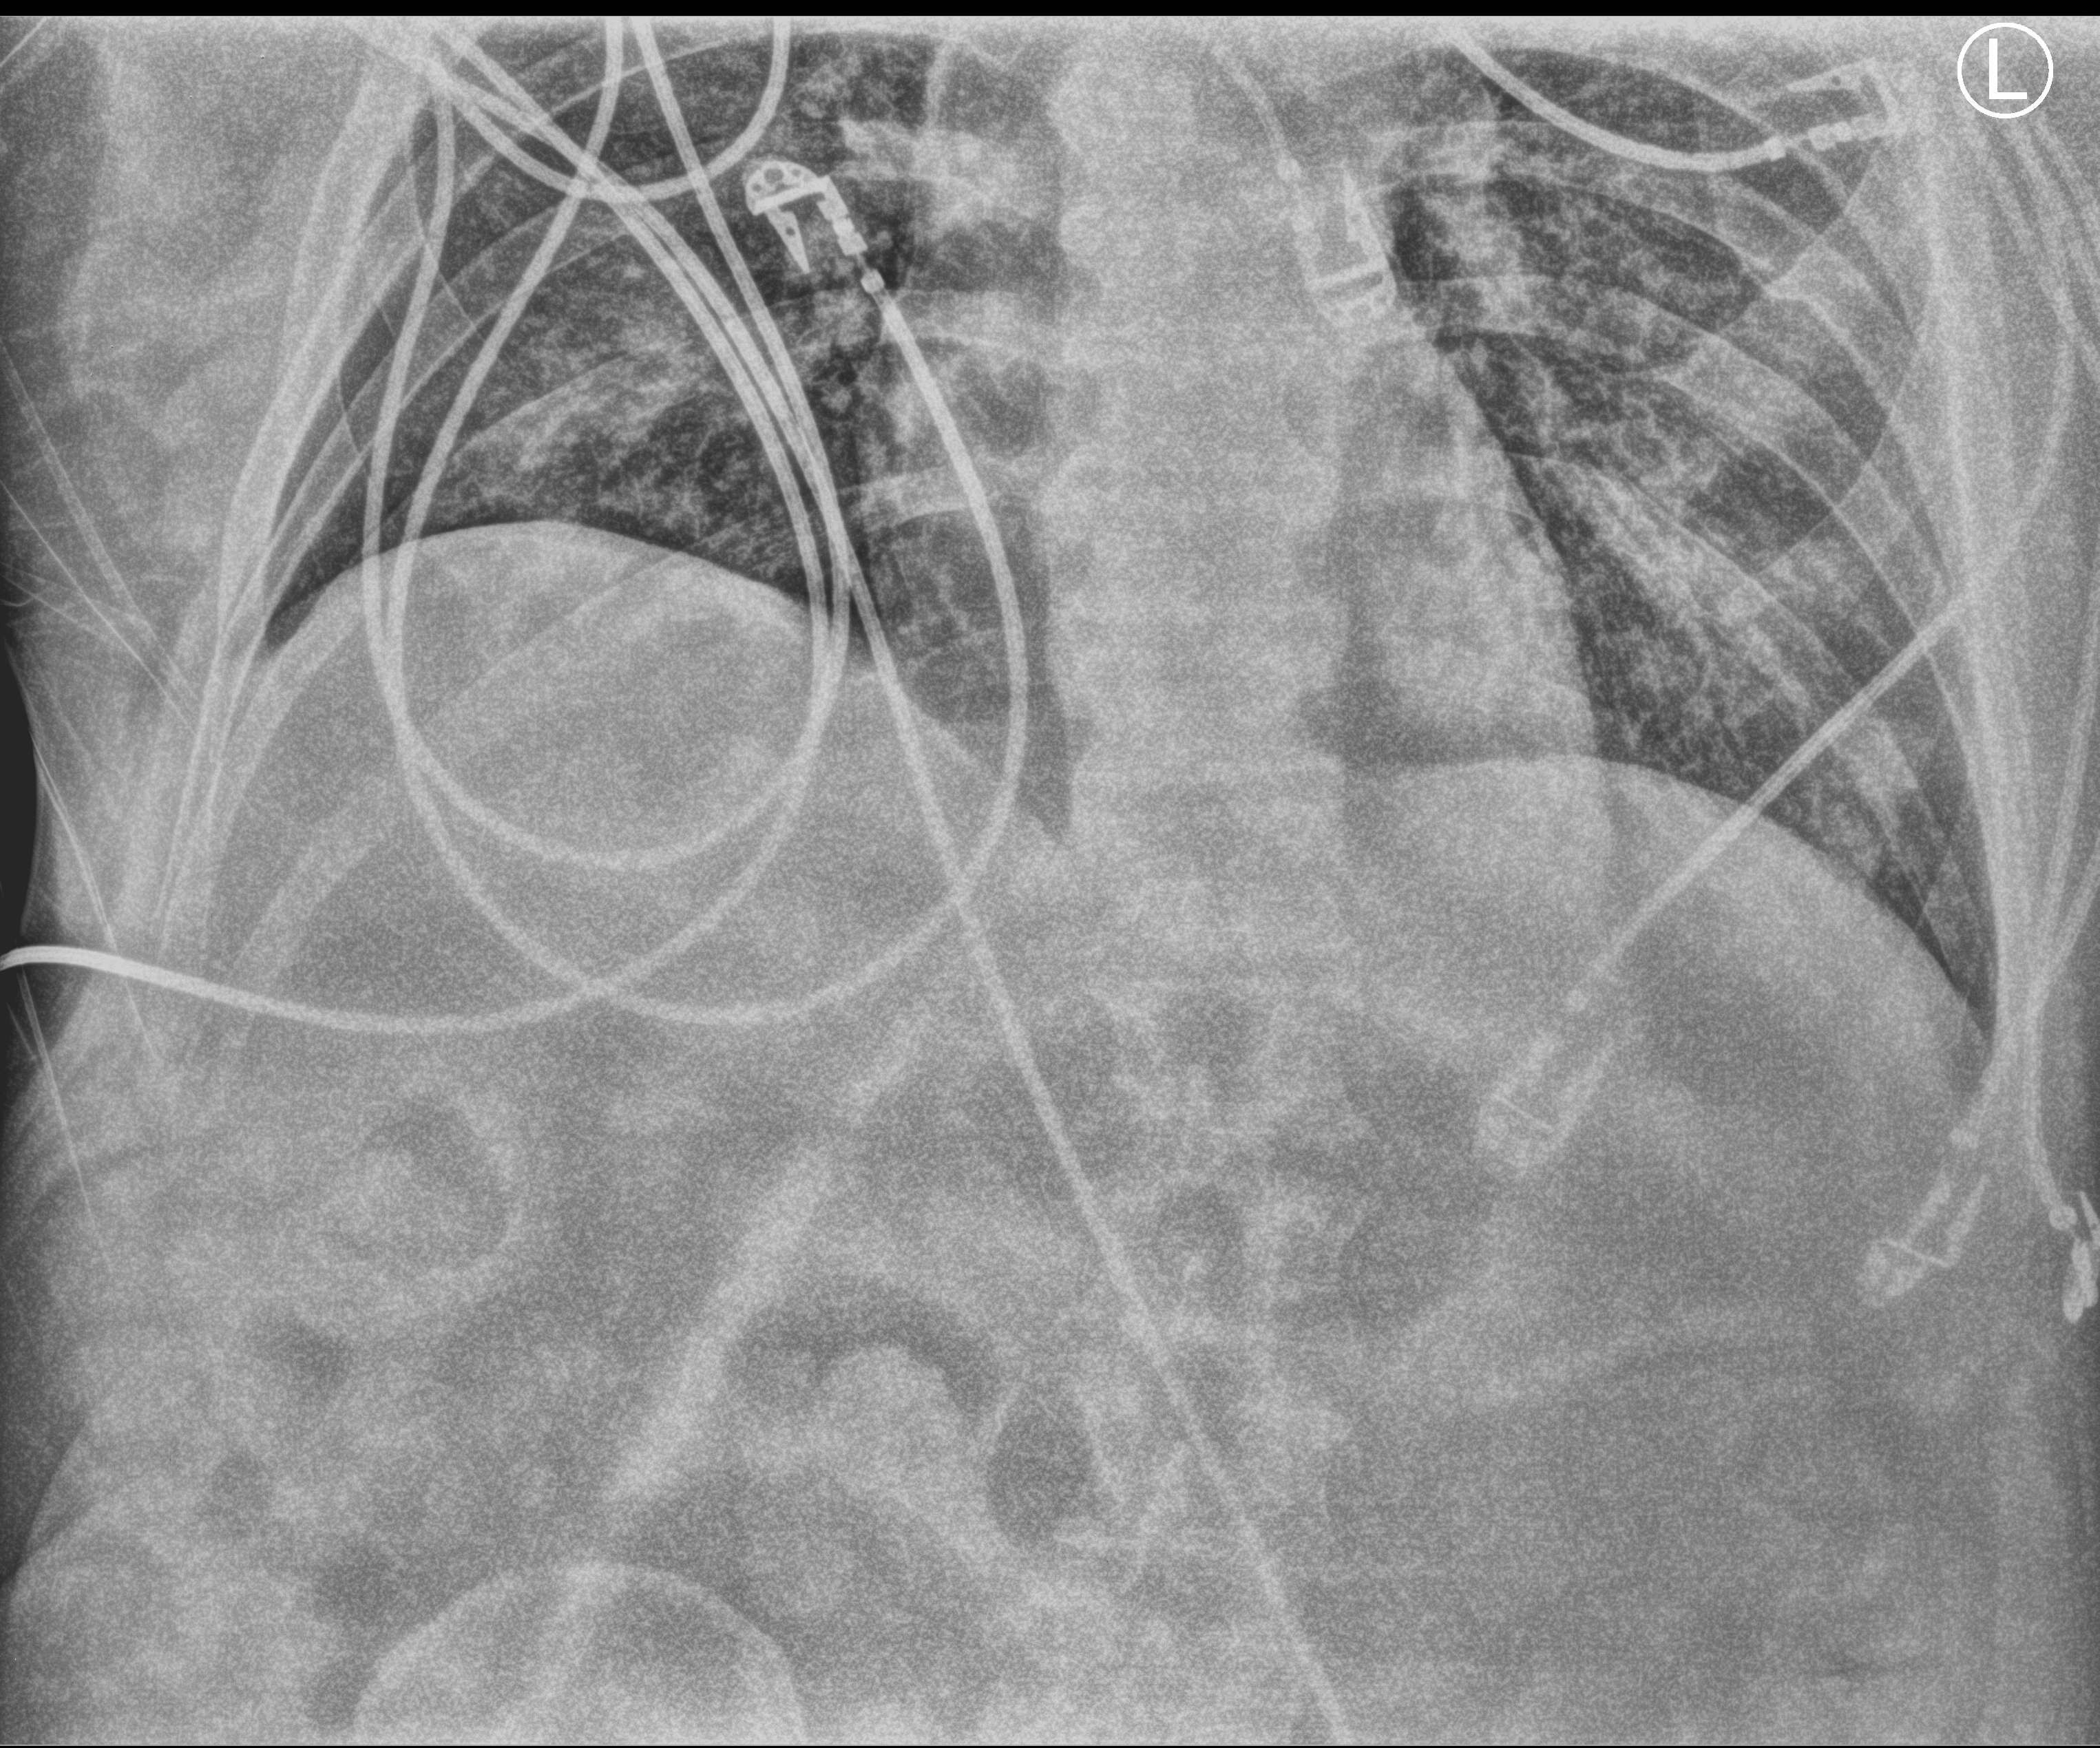
Bedside chest radiograph (computed radiography), anteroposterior (AP) projection. Adult patient hospitalised with COVID-19, age 18–59 years.
Hospital-stay facts (about this admission, not read from this image; timing relative to this image not recorded): mechanically ventilated during this hospital stay: yes; hypertension (admission record): no.